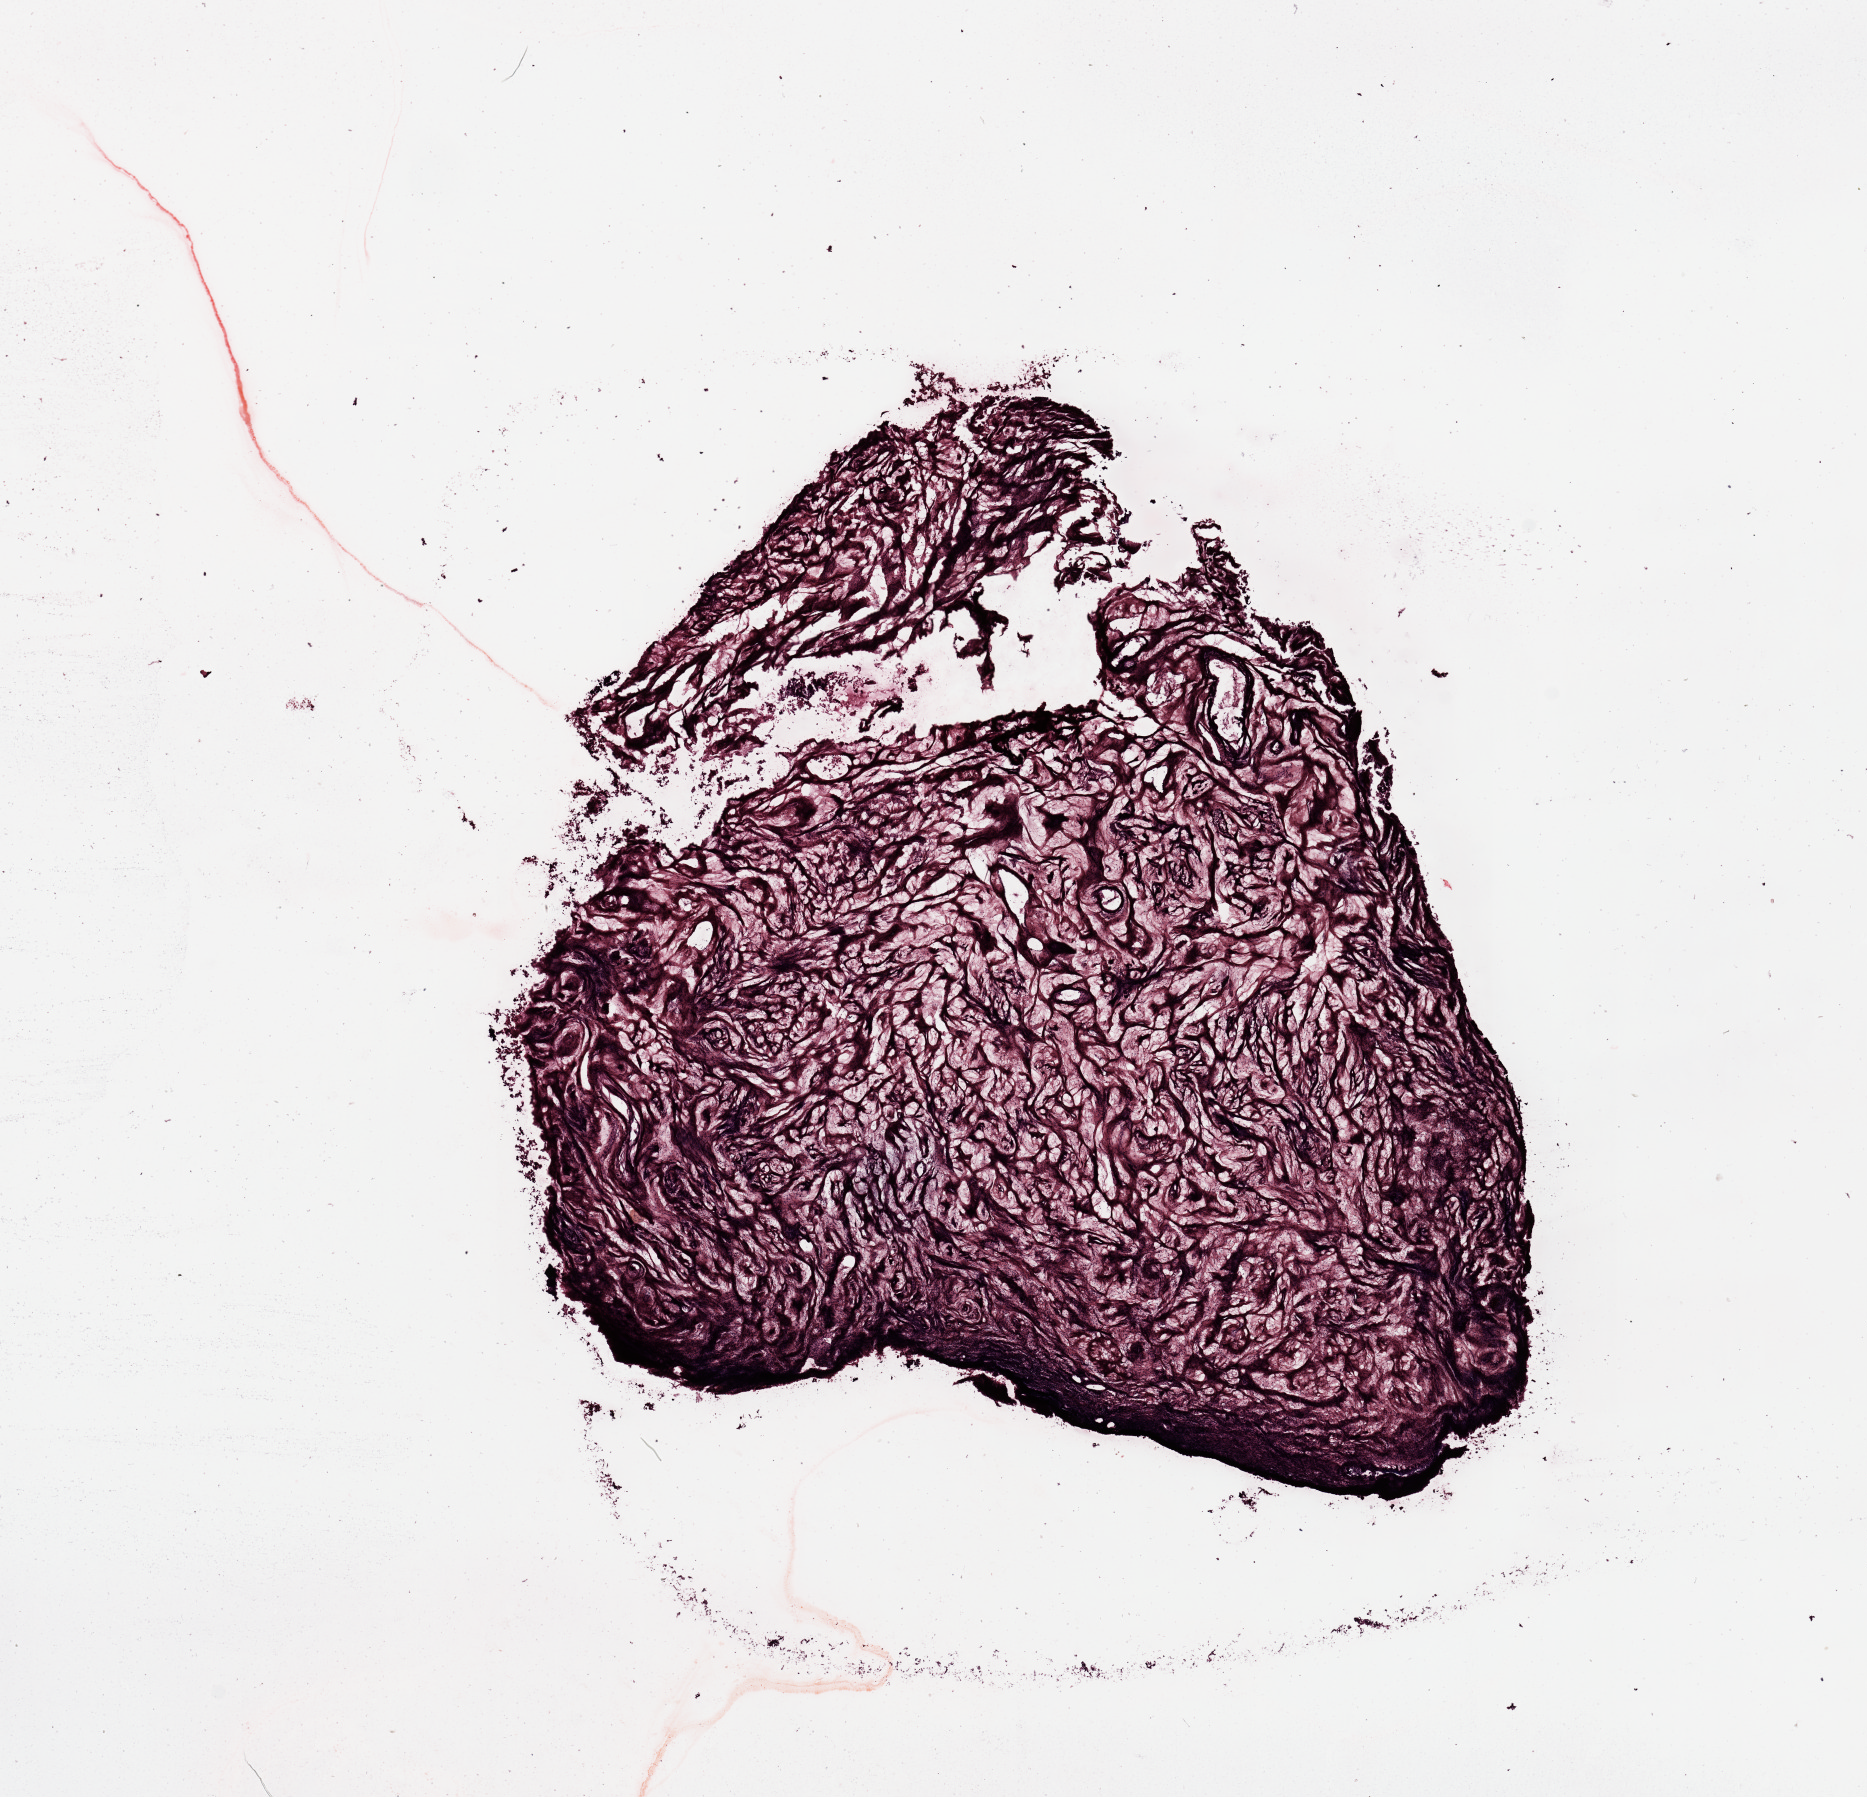
Digitized Hematoxylin and eosin (H&E) stained tissue section (whole slide), whole scanned area (about 14.8 x 14.2 mm) shown as a low-resolution overview. Uterus, normal (non-tumour) tissue. 78-year-old female patient.
This section: normal (non-tumour) tissue from the same patient. Patient diagnosis: Endometrioid adenocarcinoma, NOS.